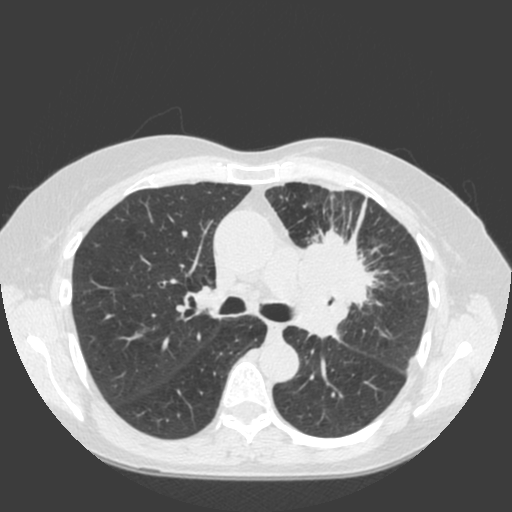
Chest CT (low-dose screening protocol), one axial image; first (baseline) screen; lung window (W 1500 / L -600 HU); 2 mm slice thickness; standard (soft-tissue) reconstruction kernel (C); 120 kVp; slice 64 of 184 in the series. Female participant, aged 66 years at enrolment. Current smoker at enrolment.
• Expert-annotated lung lesion, bounding box <280,216,400,324> (left, top, right, bottom; pixels).
• Reader record for this screening exam (exam-level; its link to the box is not recorded): non-calcified nodule or mass ≥4 mm, left upper lobe, 61 × 45 mm, spiculated (stellate) margins, soft tissue attenuation.
• Later outcome: lung cancer diagnosed 19 days after this screen — squamous cell carcinoma, keratinizing, NOS, left upper lobe, left hilum, mediastinum, left main stem bronchus, other location, poorly differentiated (G3), stage IIIB (AJCC 6th edition), 60 mm at pathology.